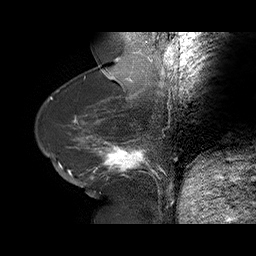
Breast MRI (dynamic contrast-enhanced), one sagittal slice. Position 25 of 75 along the scan axis. Dynamic contrast-enhanced series, time point 2 of 6 at this slice position (early post-contrast). 1.5 T. TE 4.5 ms, TR 32.4 ms. 3 mm slice thickness. 256 × 256 image matrix. Female patient. From the clinical record (not read from this slice): setting: breast cancer imaged before/during neoadjuvant chemotherapy; receptor status: HR-positive, HER2-negative.
Annotated regions visible in this slice (semi-automatically segmented with operator editing):
- analysis volume of interest (the breast-tissue region the enhancement analysis was run in; not a lesion): bounding box (x1, y1, x2, y2) in pixels: (58, 134, 166, 191)
- tumour enhancement mask (voxels above the 100 % enhancement threshold inside the analysis volume of interest): (67, 136, 162, 191)